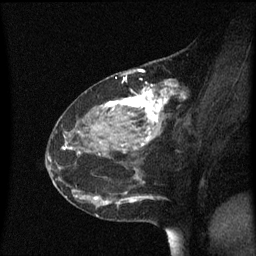
Breast MRI (dynamic contrast-enhanced), one sagittal slice. Position 27 of 60 along the scan axis. Dynamic contrast-enhanced series, image 2 of 3 at this slice position (ordered by acquisition). 1.5 T. TE 4.2 ms, TR 8.4 ms. 2 mm slice thickness. 256 × 256 image matrix. Patient: female, 48 years. From the clinical record (not read from this slice): setting: breast cancer imaged before/during neoadjuvant chemotherapy; receptor status: HR-positive, HER2-negative.
Outlined on this slice (semi-automatically segmented with operator editing):
- analysis volume of interest (the breast-tissue region the enhancement analysis was run in; not a lesion): bounding box [x1, y1, x2, y2] px = [80, 78, 191, 221]
- tumour enhancement mask (voxels above the 70 % enhancement threshold inside the analysis volume of interest): [96, 82, 185, 203]